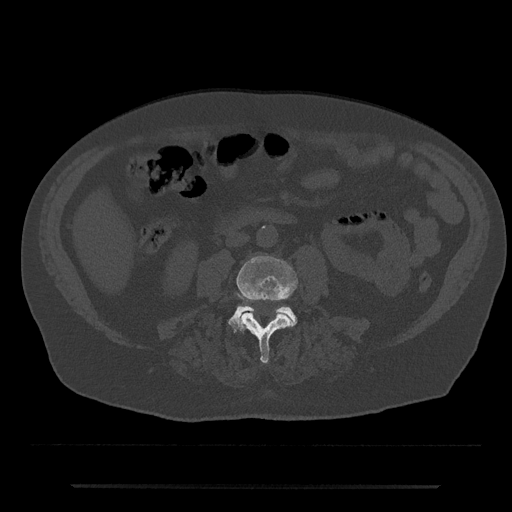
CT including the spine, one axial slice; slice 388 of 797 in the series (ordered by position); 120 kVp; bone window (W 1800 / L 400 HU); 0.5 mm slice thickness; 512 × 512 image matrix. Patient: male, 80 years. From the clinical record (not read from this slice): primary cancer: prostate.
Outlined on this slice (semi-automatically segmented with operator editing):
- L3 vertebra: bounding box <236,256,298,363> (left, top, right, bottom; pixels)
- L4 vertebra: <228,305,298,331>